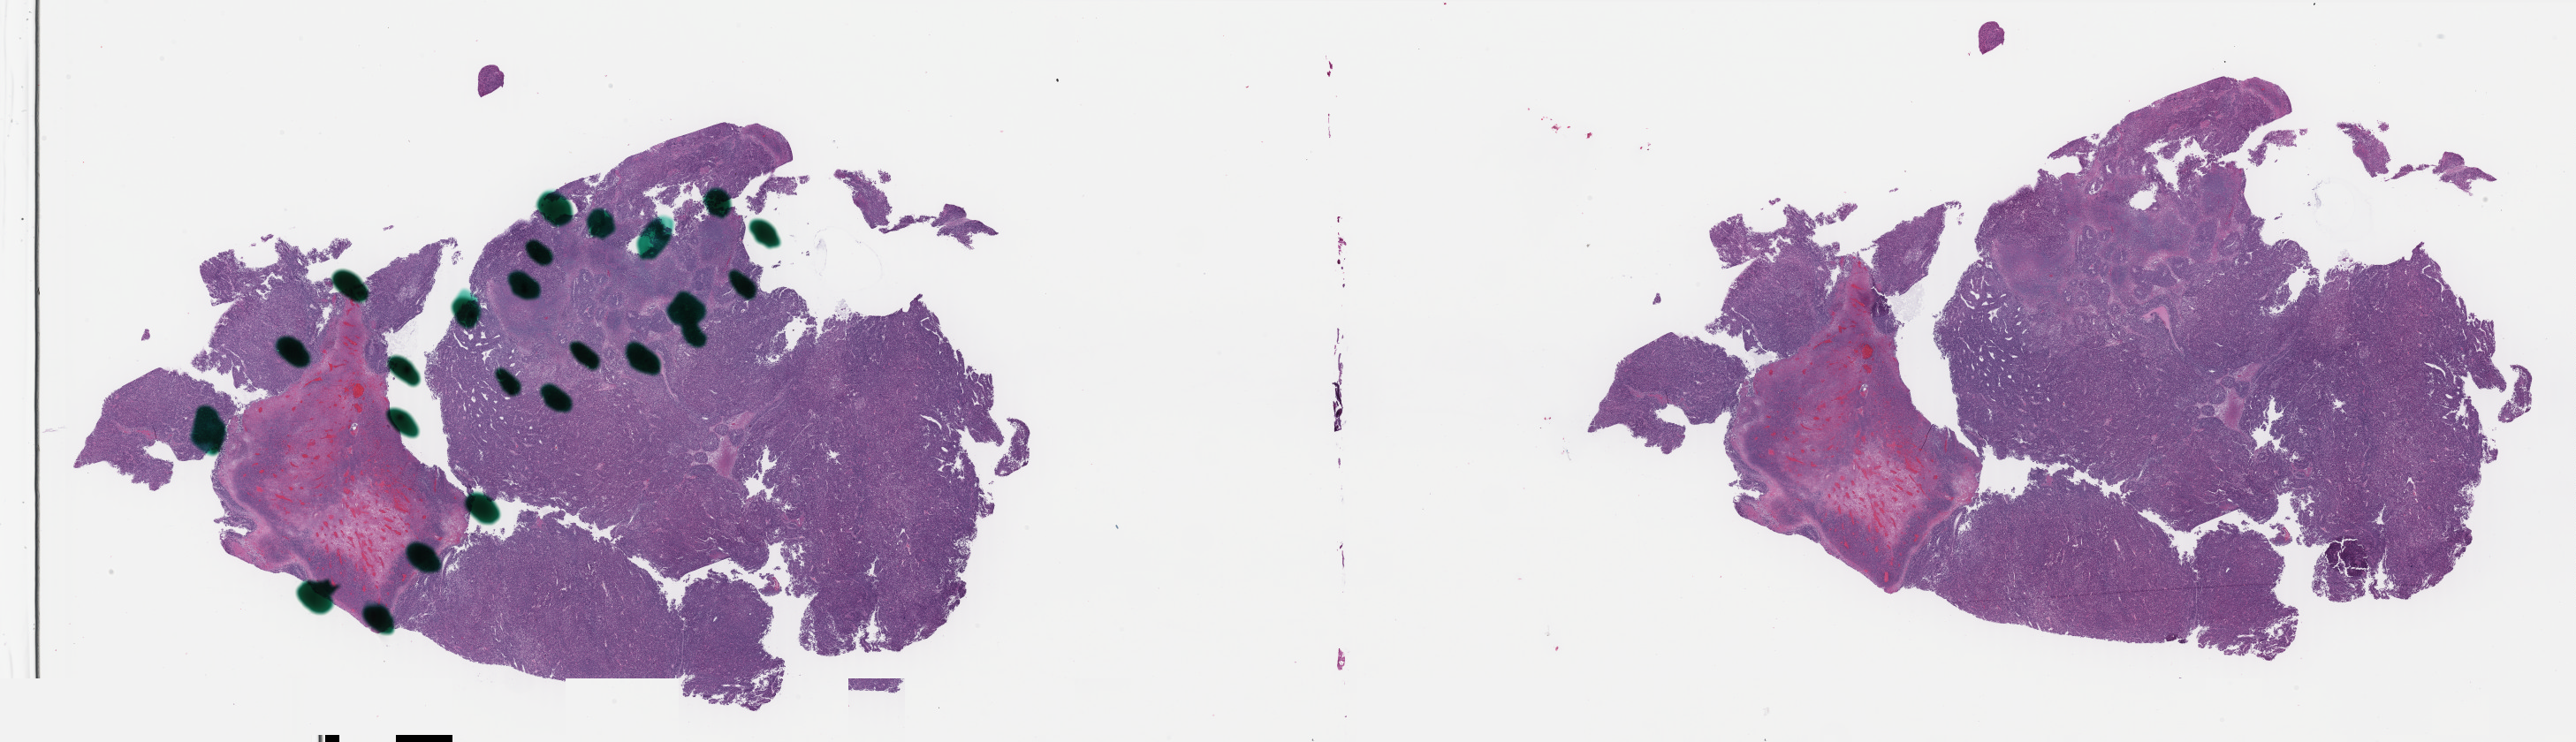
Whole-slide histology image, H&E — whole scanned area (about 46.1 x 13.3 mm, slide scanned at 40x) shown as a low-resolution overview, FFPE section, liver, primary tumour sample. Female, age 66 years at initial diagnosis. Histologic grade: G3 (poorly differentiated).
TNM: T4 N0 M0. AJCC pathologic stage: IIIC (7th edition). Pathologic diagnosis: Hepatocellular carcinoma, NOS.